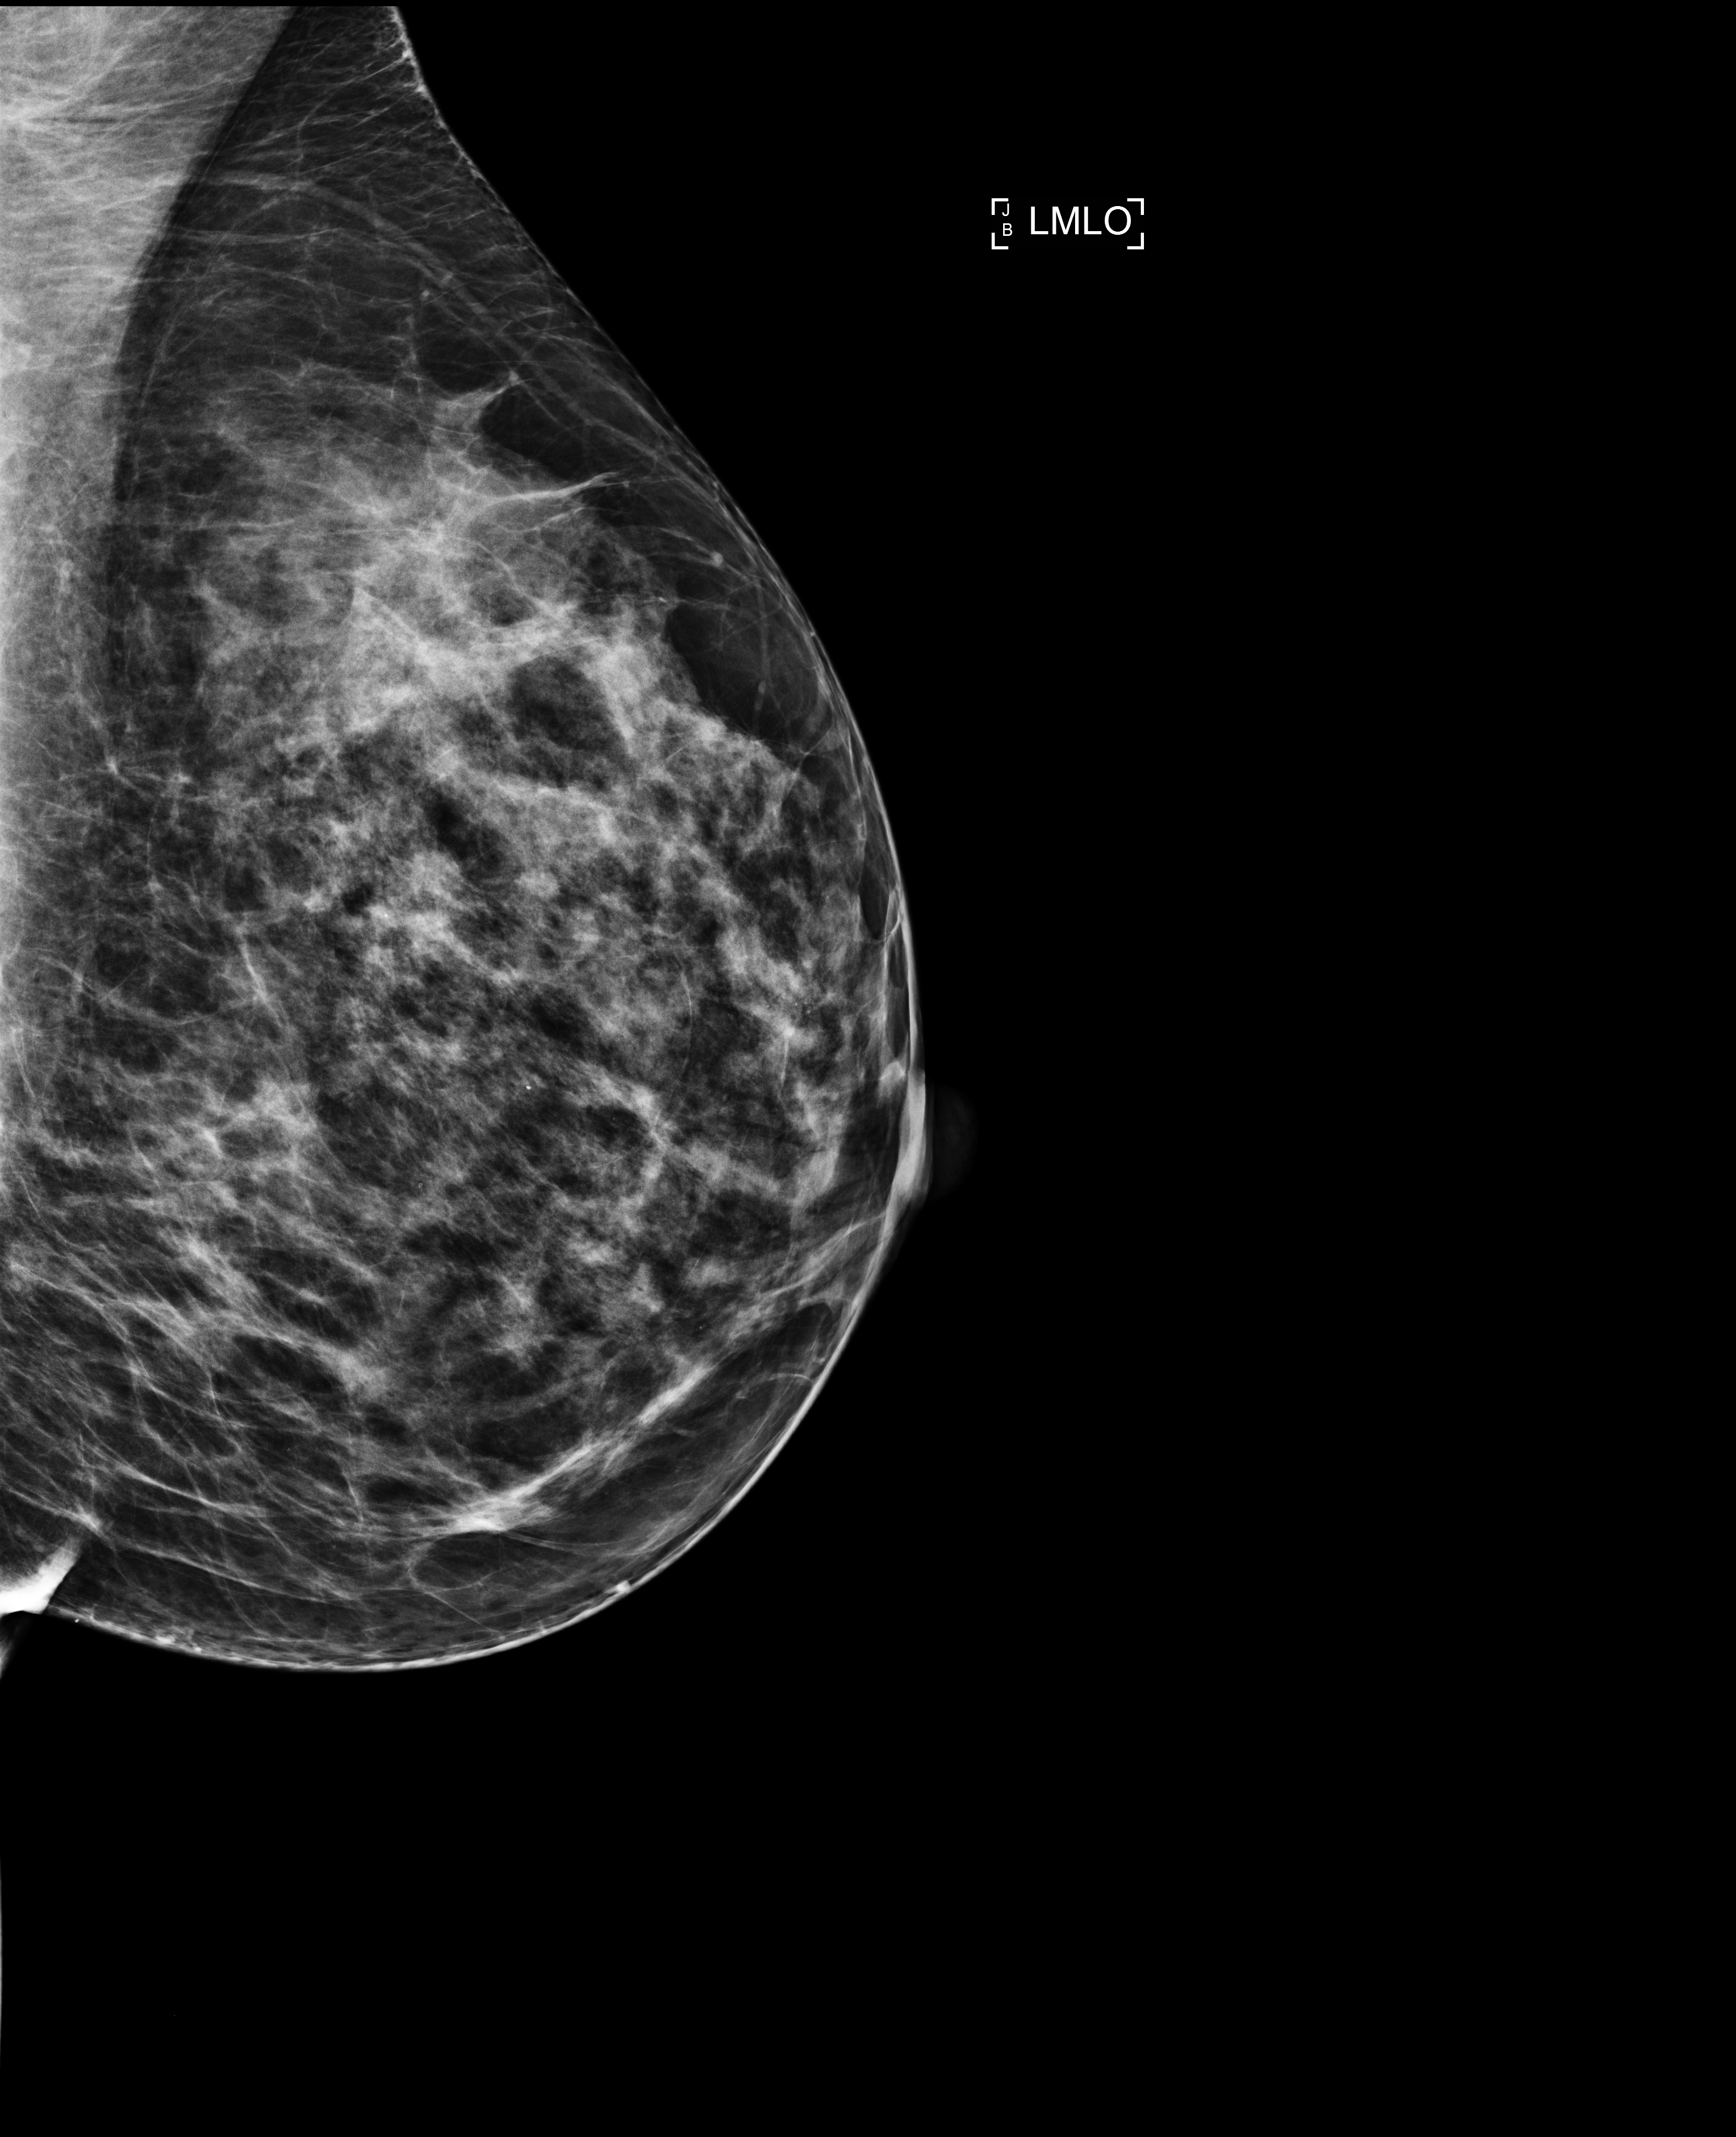
Digital mammogram (FFDM), left breast, mediolateral oblique (MLO) view, screening examination. Female patient, age 47 years.
BI-RADS breast density category at the screening exam (both breasts, scale 1–4): 3. Final BI-RADS assessment for this screening round (tomosynthesis exam, both breasts): category 1. Recall: no recall after this screen.